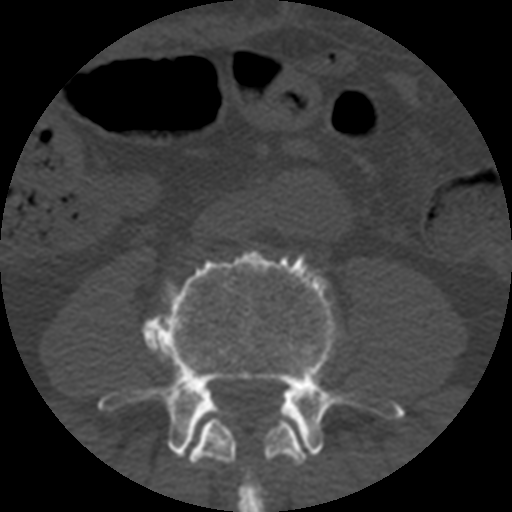
CT including the spine, one axial slice. Slice 100 of 508 in the series (ordered by position). Bone window (W 1800 / L 400 HU). 1.25 mm slice thickness. 512 × 512 image matrix. Patient age 57 years. From the clinical record (not read from this slice): primary cancer: prostate.
Outlined on this slice (semi-automatically segmented with operator editing):
- L3 vertebra: bounding box (x1, y1, x2, y2) in pixels: (189, 417, 306, 512)
- L4 vertebra: (98, 249, 404, 458)